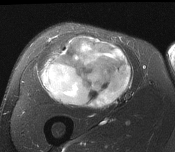
MRI of an extremity soft-tissue mass, one axial slice. Position 92 of 116 along the scan axis. T2-weighted fat-saturated. MR volume resampled by the dataset authors to the PET/CT grid (not the native acquisition matrix). 3.27 mm slice thickness. 175 × 152 image matrix. Male patient. Case-level facts recorded for this patient, not image findings: histological type: pleiomorphic leiomyosarcoma; grade: intermediate; site of the primary tumour: right thigh.
Structures marked on this image (expert contour drawn on MRI and transferred to this co-registered scan by the dataset authors):
- gross tumour volume including surrounding oedema: bounding box <40,38,132,109> (left, top, right, bottom; pixels)
- gross tumour volume (mass): <42,38,132,109>